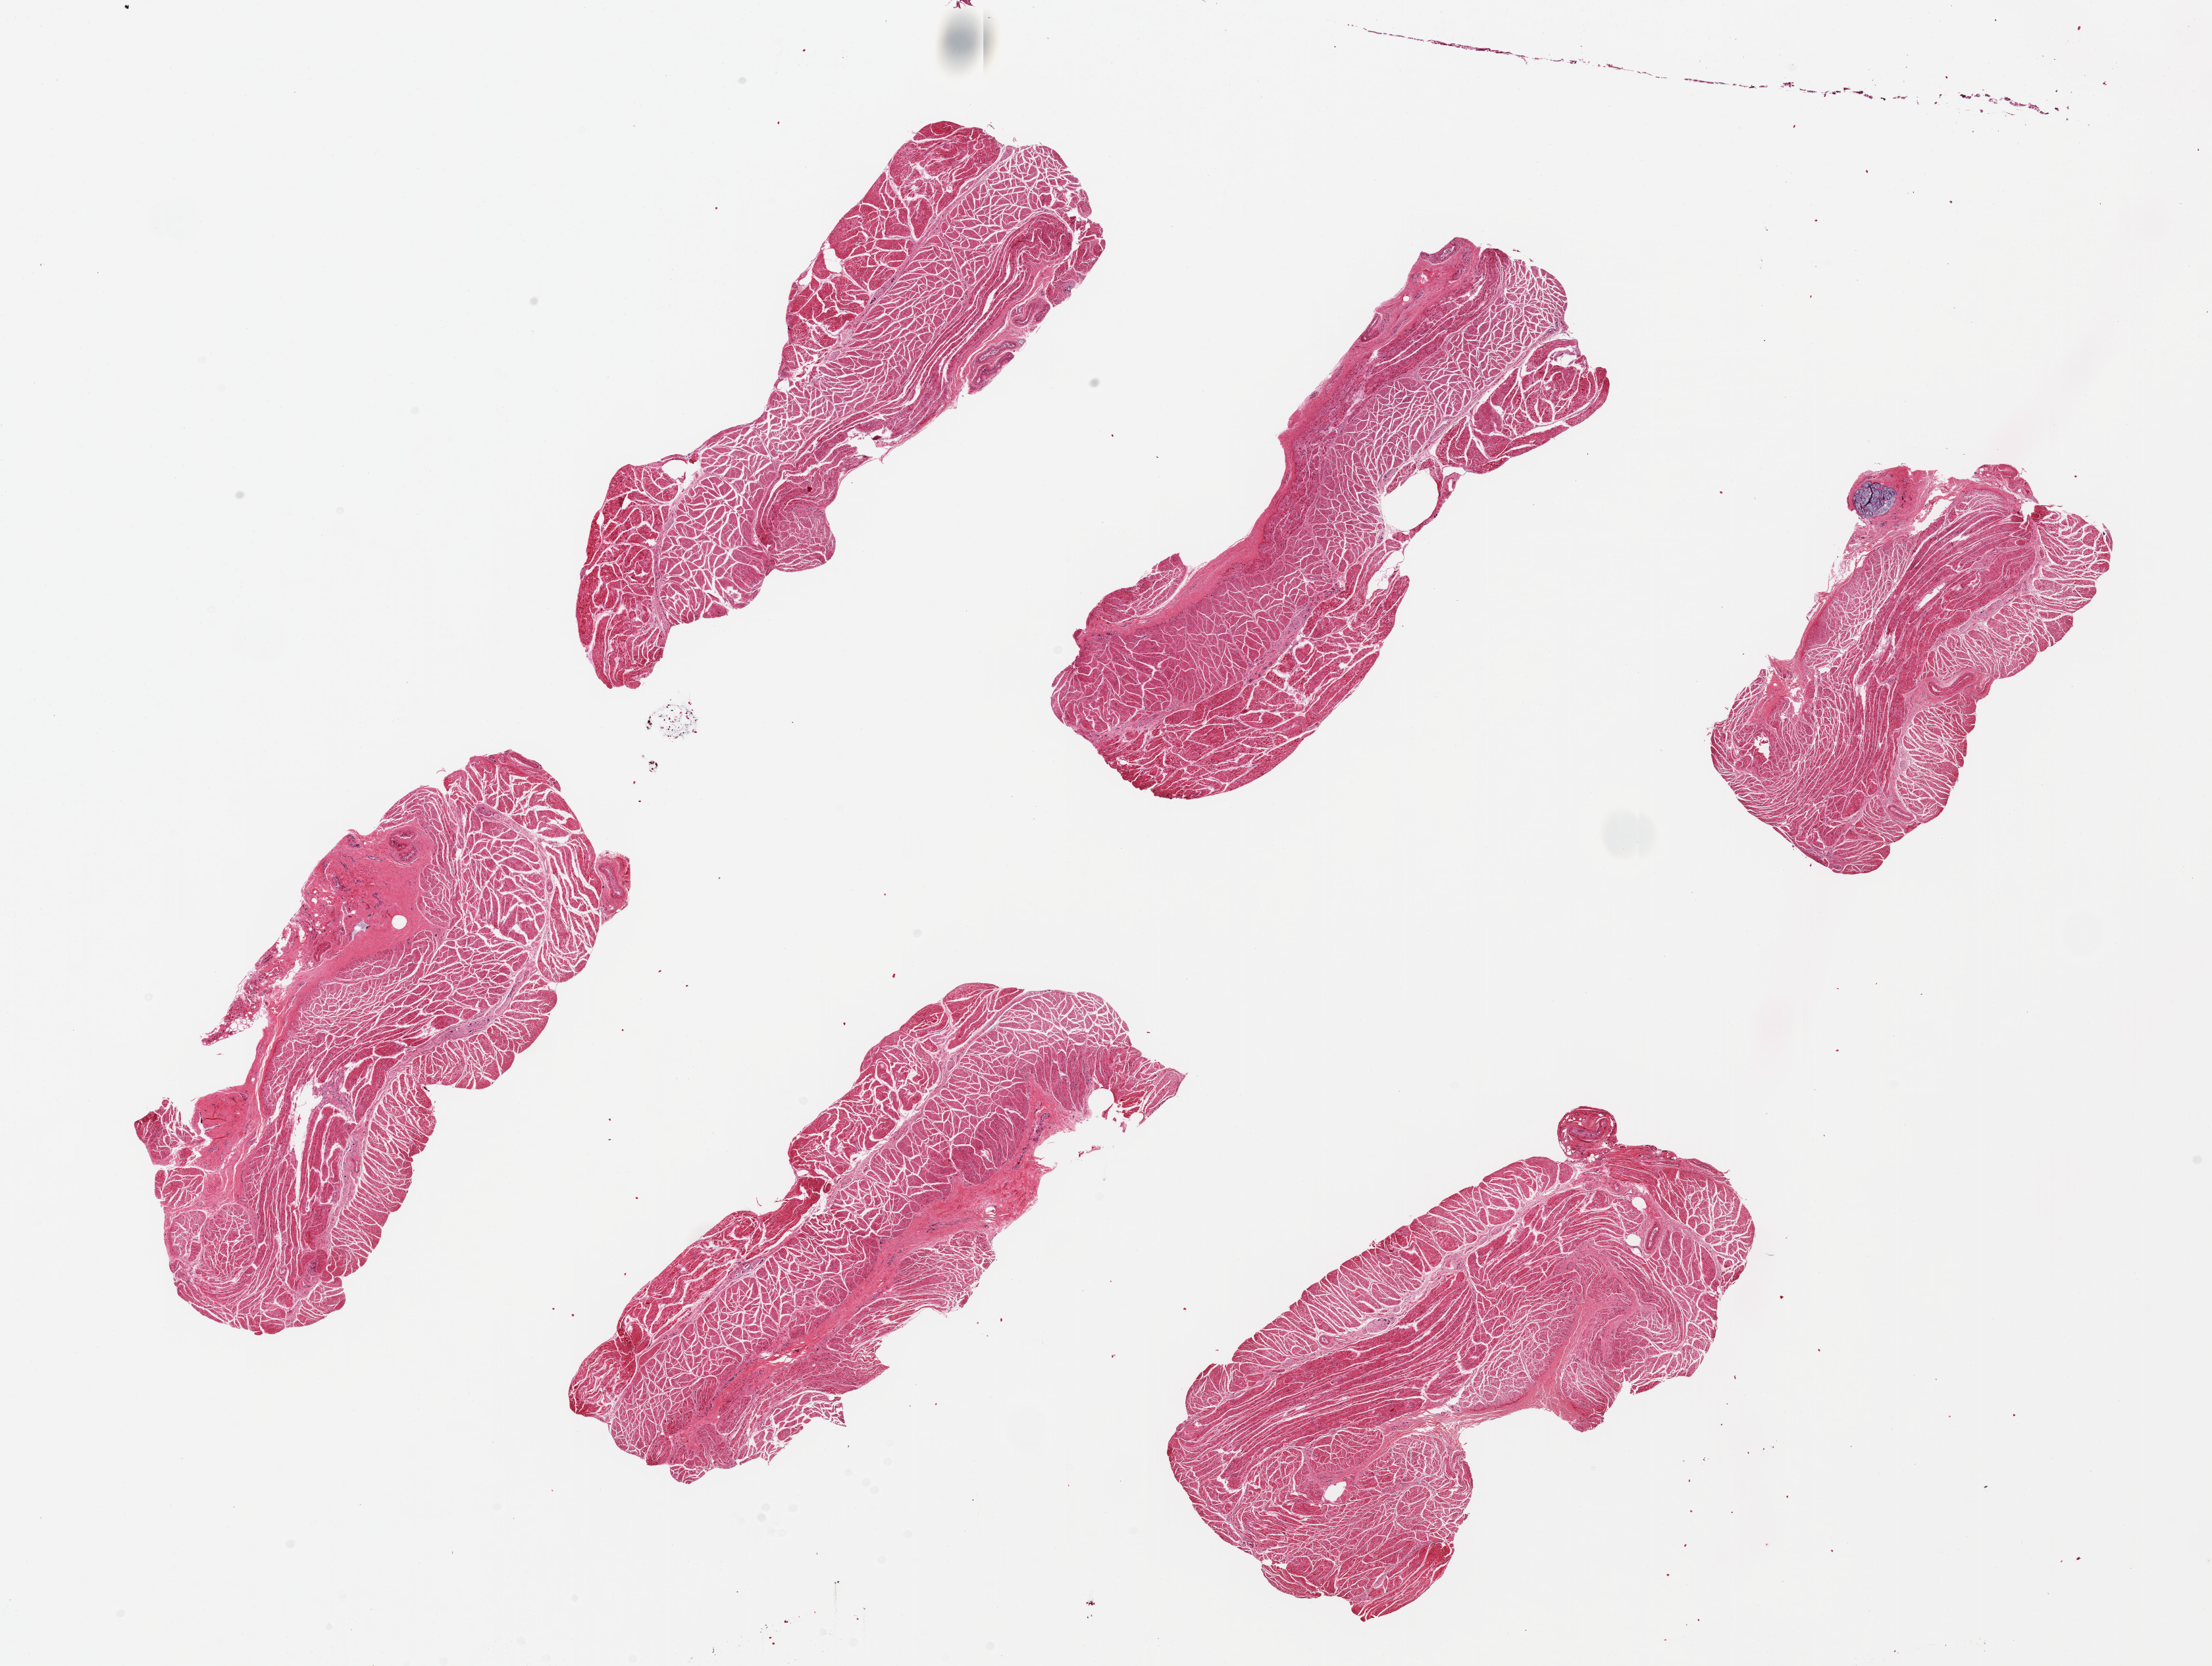
H&E whole-slide image — low-resolution overview of the scanned area, about 26.6 x 20.0 mm; PAXgene-fixed, paraffin-embedded tissue; section of esophageal muscle (target tissue); donor tissue sample. Donor sex: male.
Review note (as recorded): 6 pieces, up to 8x3mm; Well trimmed, muscularis free of adipose.